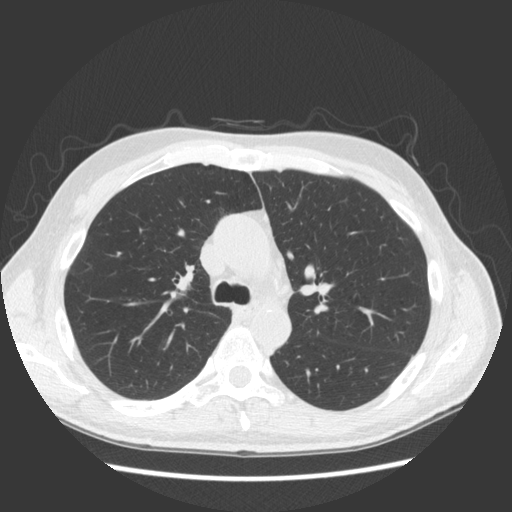
Low-dose screening chest CT, axial slice, second screening round (one year after baseline), lung window (W 1500 / L -600 HU), 2.5 mm slice thickness, standard (soft-tissue) reconstruction kernel (STANDARD), 120 kVp. Male, age 57 years at enrolment.
Expert-annotated lung lesion, bounding box (x1, y1, x2, y2) in pixels: (154, 254, 204, 298). The screening reader recorded 3 non-calcified nodules or masses ≥4 mm on this exam (right middle lobe, right middle lobe, right middle lobe); which of them this box marks is not recorded. Participant outcome: lung cancer diagnosed 264 days after this screen — adenocarcinoma, NOS, right upper lobe, poorly differentiated (G3), stage IB (AJCC 6th edition), 25 mm at pathology.